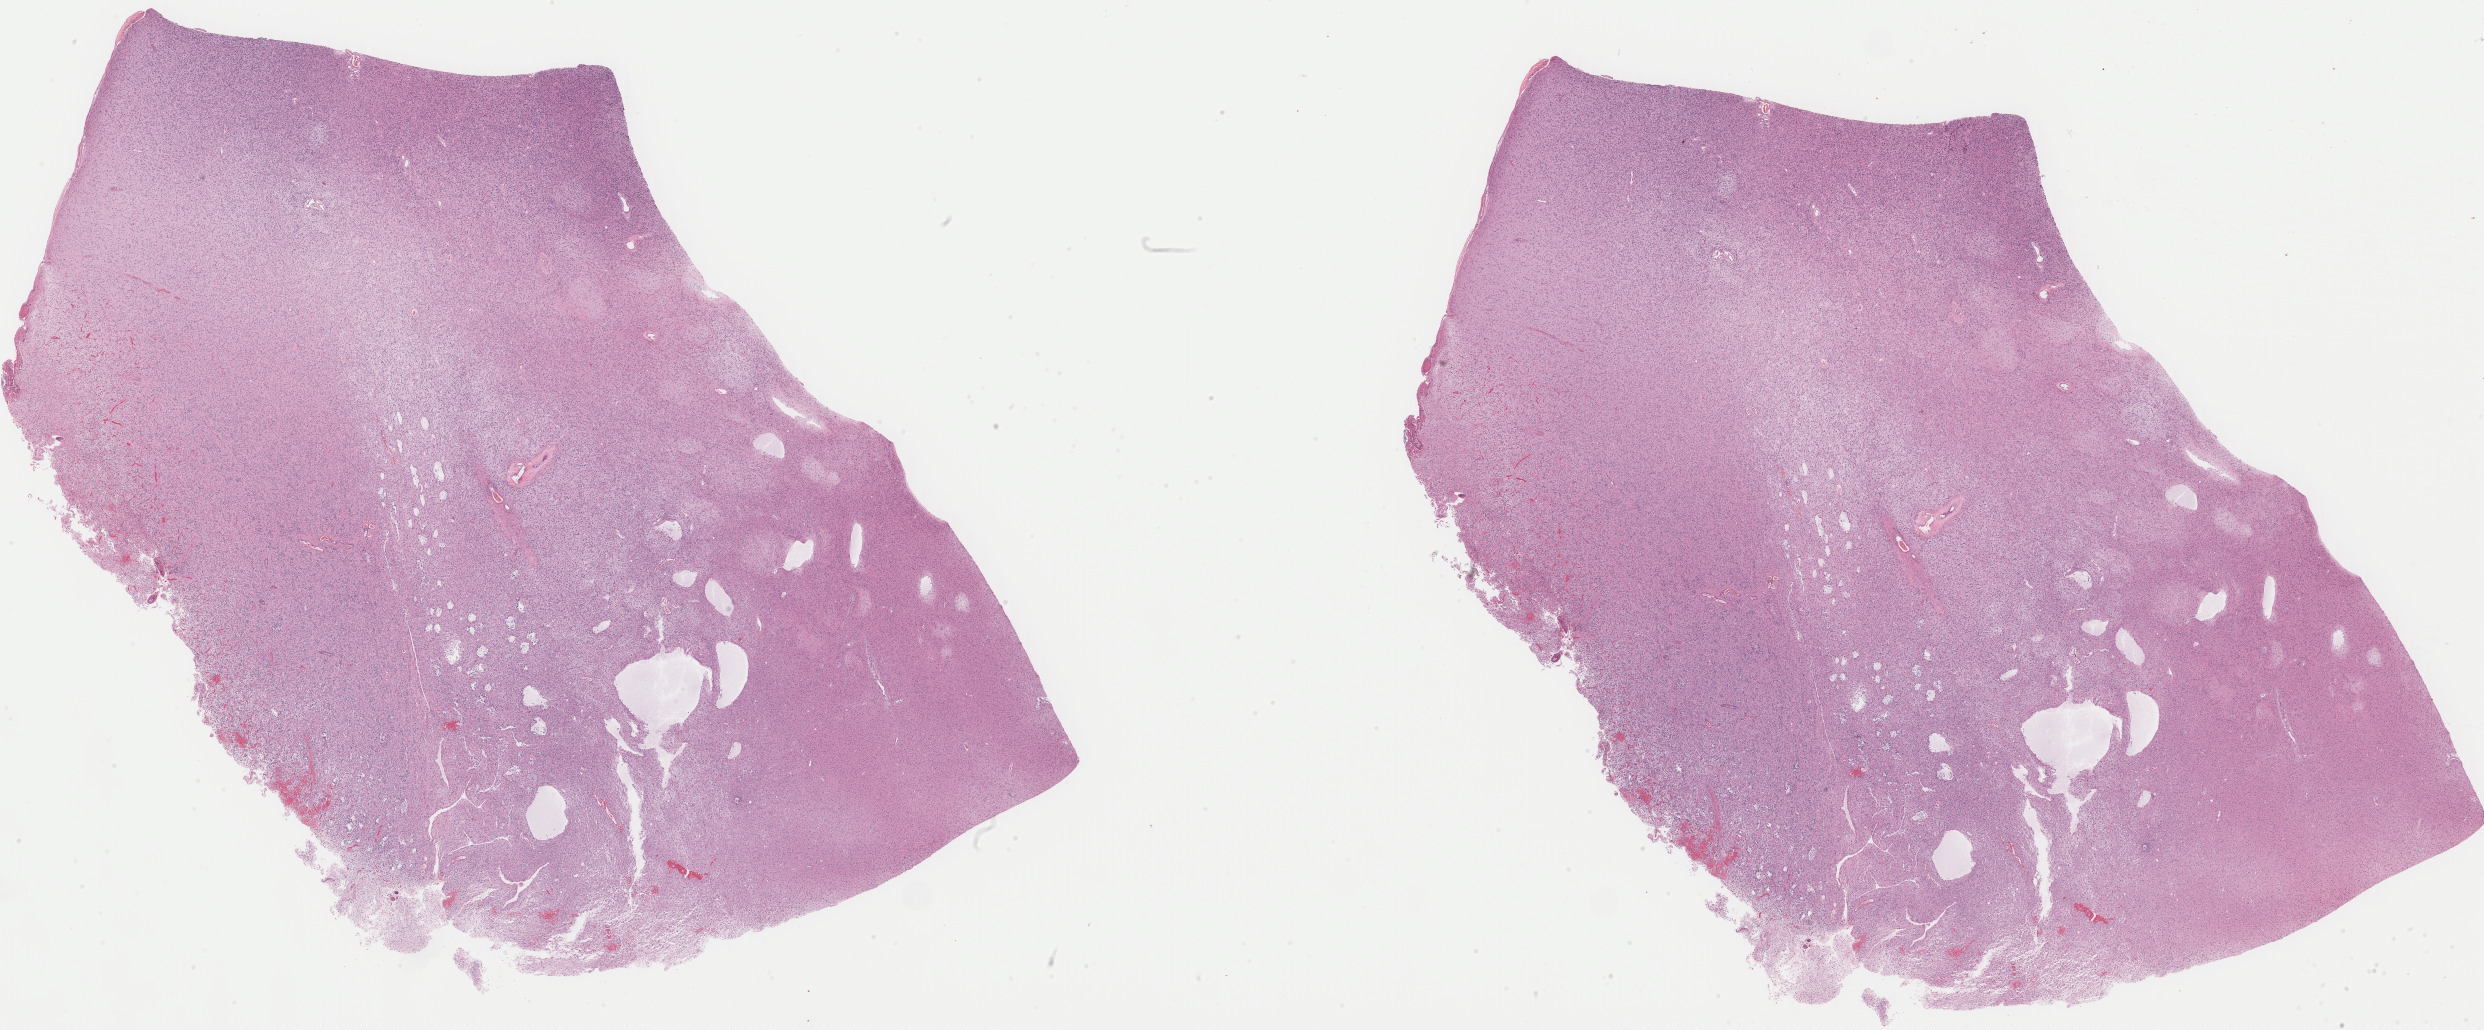
Hematoxylin and eosin (H&E) stained whole-slide image — a low-resolution overview of the entire scanned area, about 39.1 x 16.2 mm (acquisition: 40x scan). Formalin-fixed paraffin-embedded (FFPE) diagnostic section. Sample: primary tumour, brain. Female patient; age at initial diagnosis 41 years. Histologic grade: G3 (poorly differentiated).
Laterality: right. Pathologic diagnosis: Astrocytoma, anaplastic (frontal lobe).